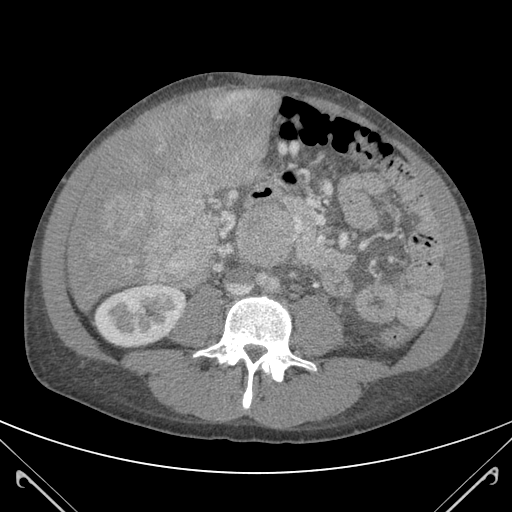
Contrast-enhanced abdominal CT (liver protocol), one axial slice. Slice 39 of 118 in the series (ordered by position). 120 kVp. Soft-tissue window (W 400 / L 40 HU). 3 mm slice thickness. 512 × 512 image matrix. From the clinical record (not read from this slice): diagnosis: hepatocellular carcinoma (patient treated with transarterial chemoembolisation; whether this scan precedes or follows treatment is not stated here); TNM stage (as recorded): Stage-IIIB; Child-Pugh class: A.
Annotated regions visible in this slice (semi-automatic segmentation, software-assisted and operator-edited):
- liver parenchyma outside the tumour (the mass and vessels are separate outlines, so this box may not span the whole liver): box from (x=68, y=90) to (x=278, y=310) px
- mass: (x=90, y=90)–(x=270, y=284)
- liver vessels: (x=200, y=201)–(x=202, y=204)